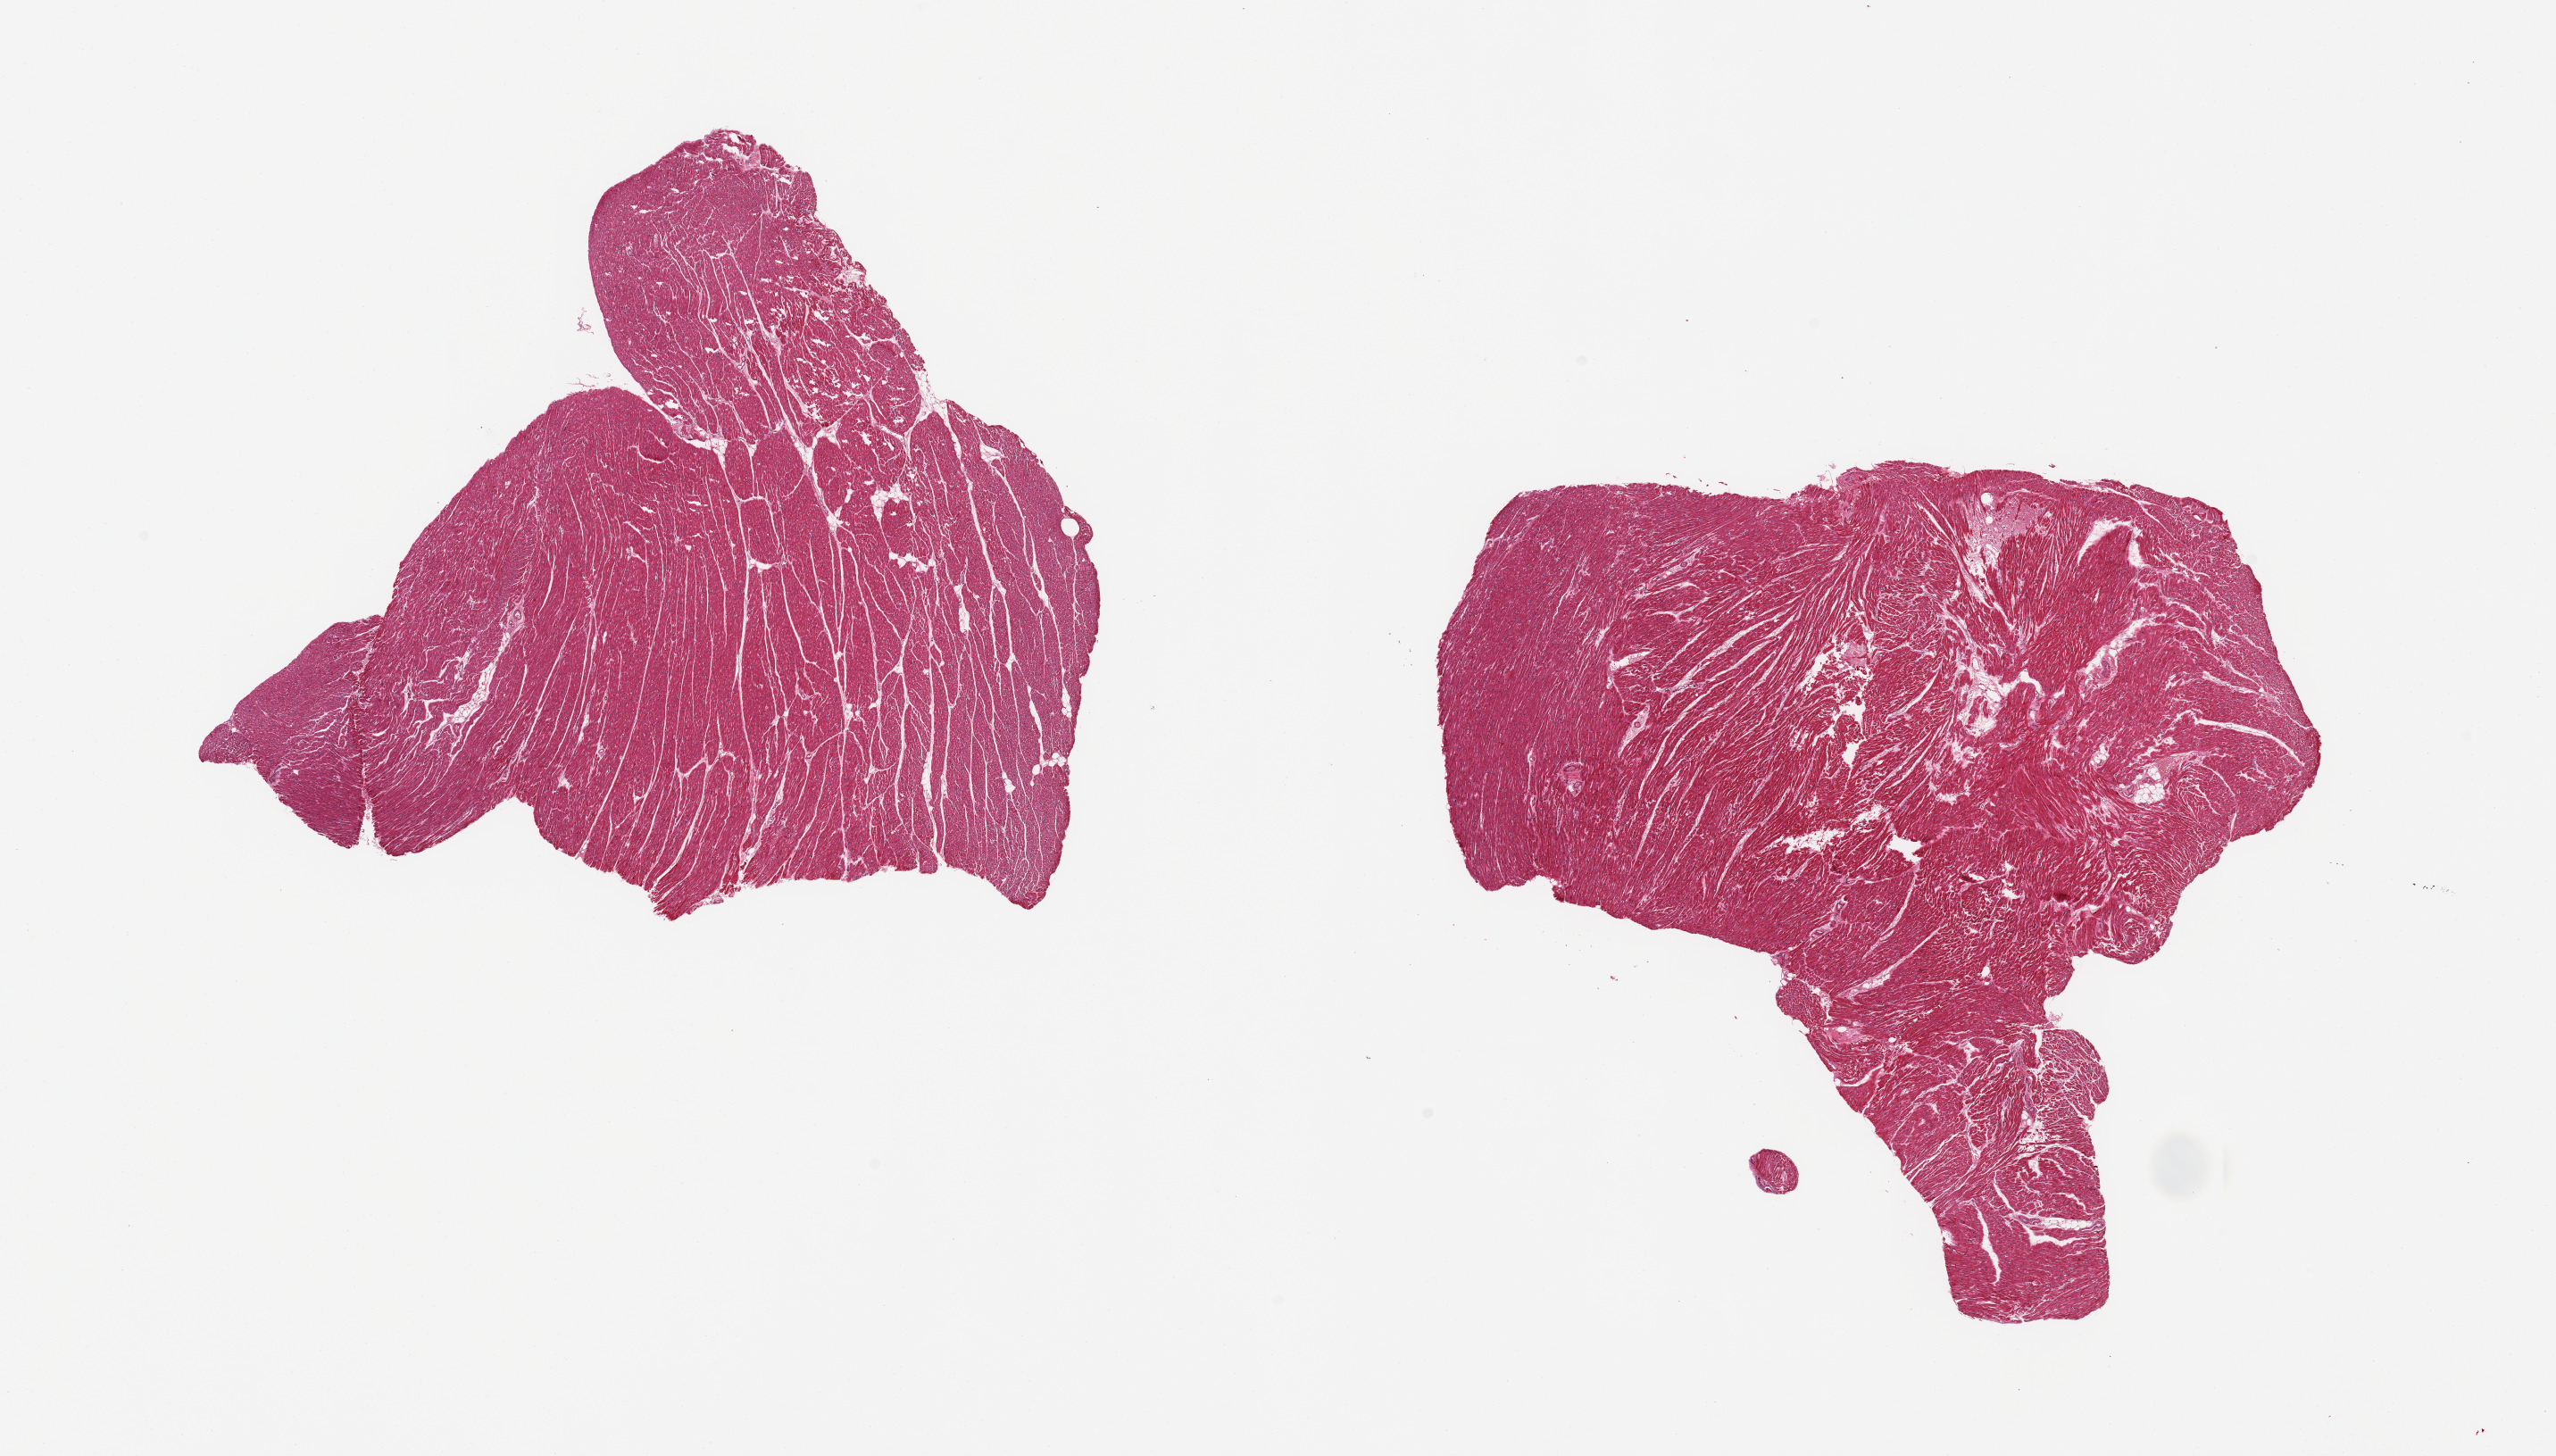
Digitized hematoxylin and eosin (H&E)-stained section, shown as a low-resolution overview of the whole scanned area (about 22.6 x 12.9 mm), PAXgene-fixed paraffin-embedded (PFPE) section, section of heart (target tissue), donor tissue sample. Donor: female.
Pathologist's review note for this sample: 2 pieces; no infarct.